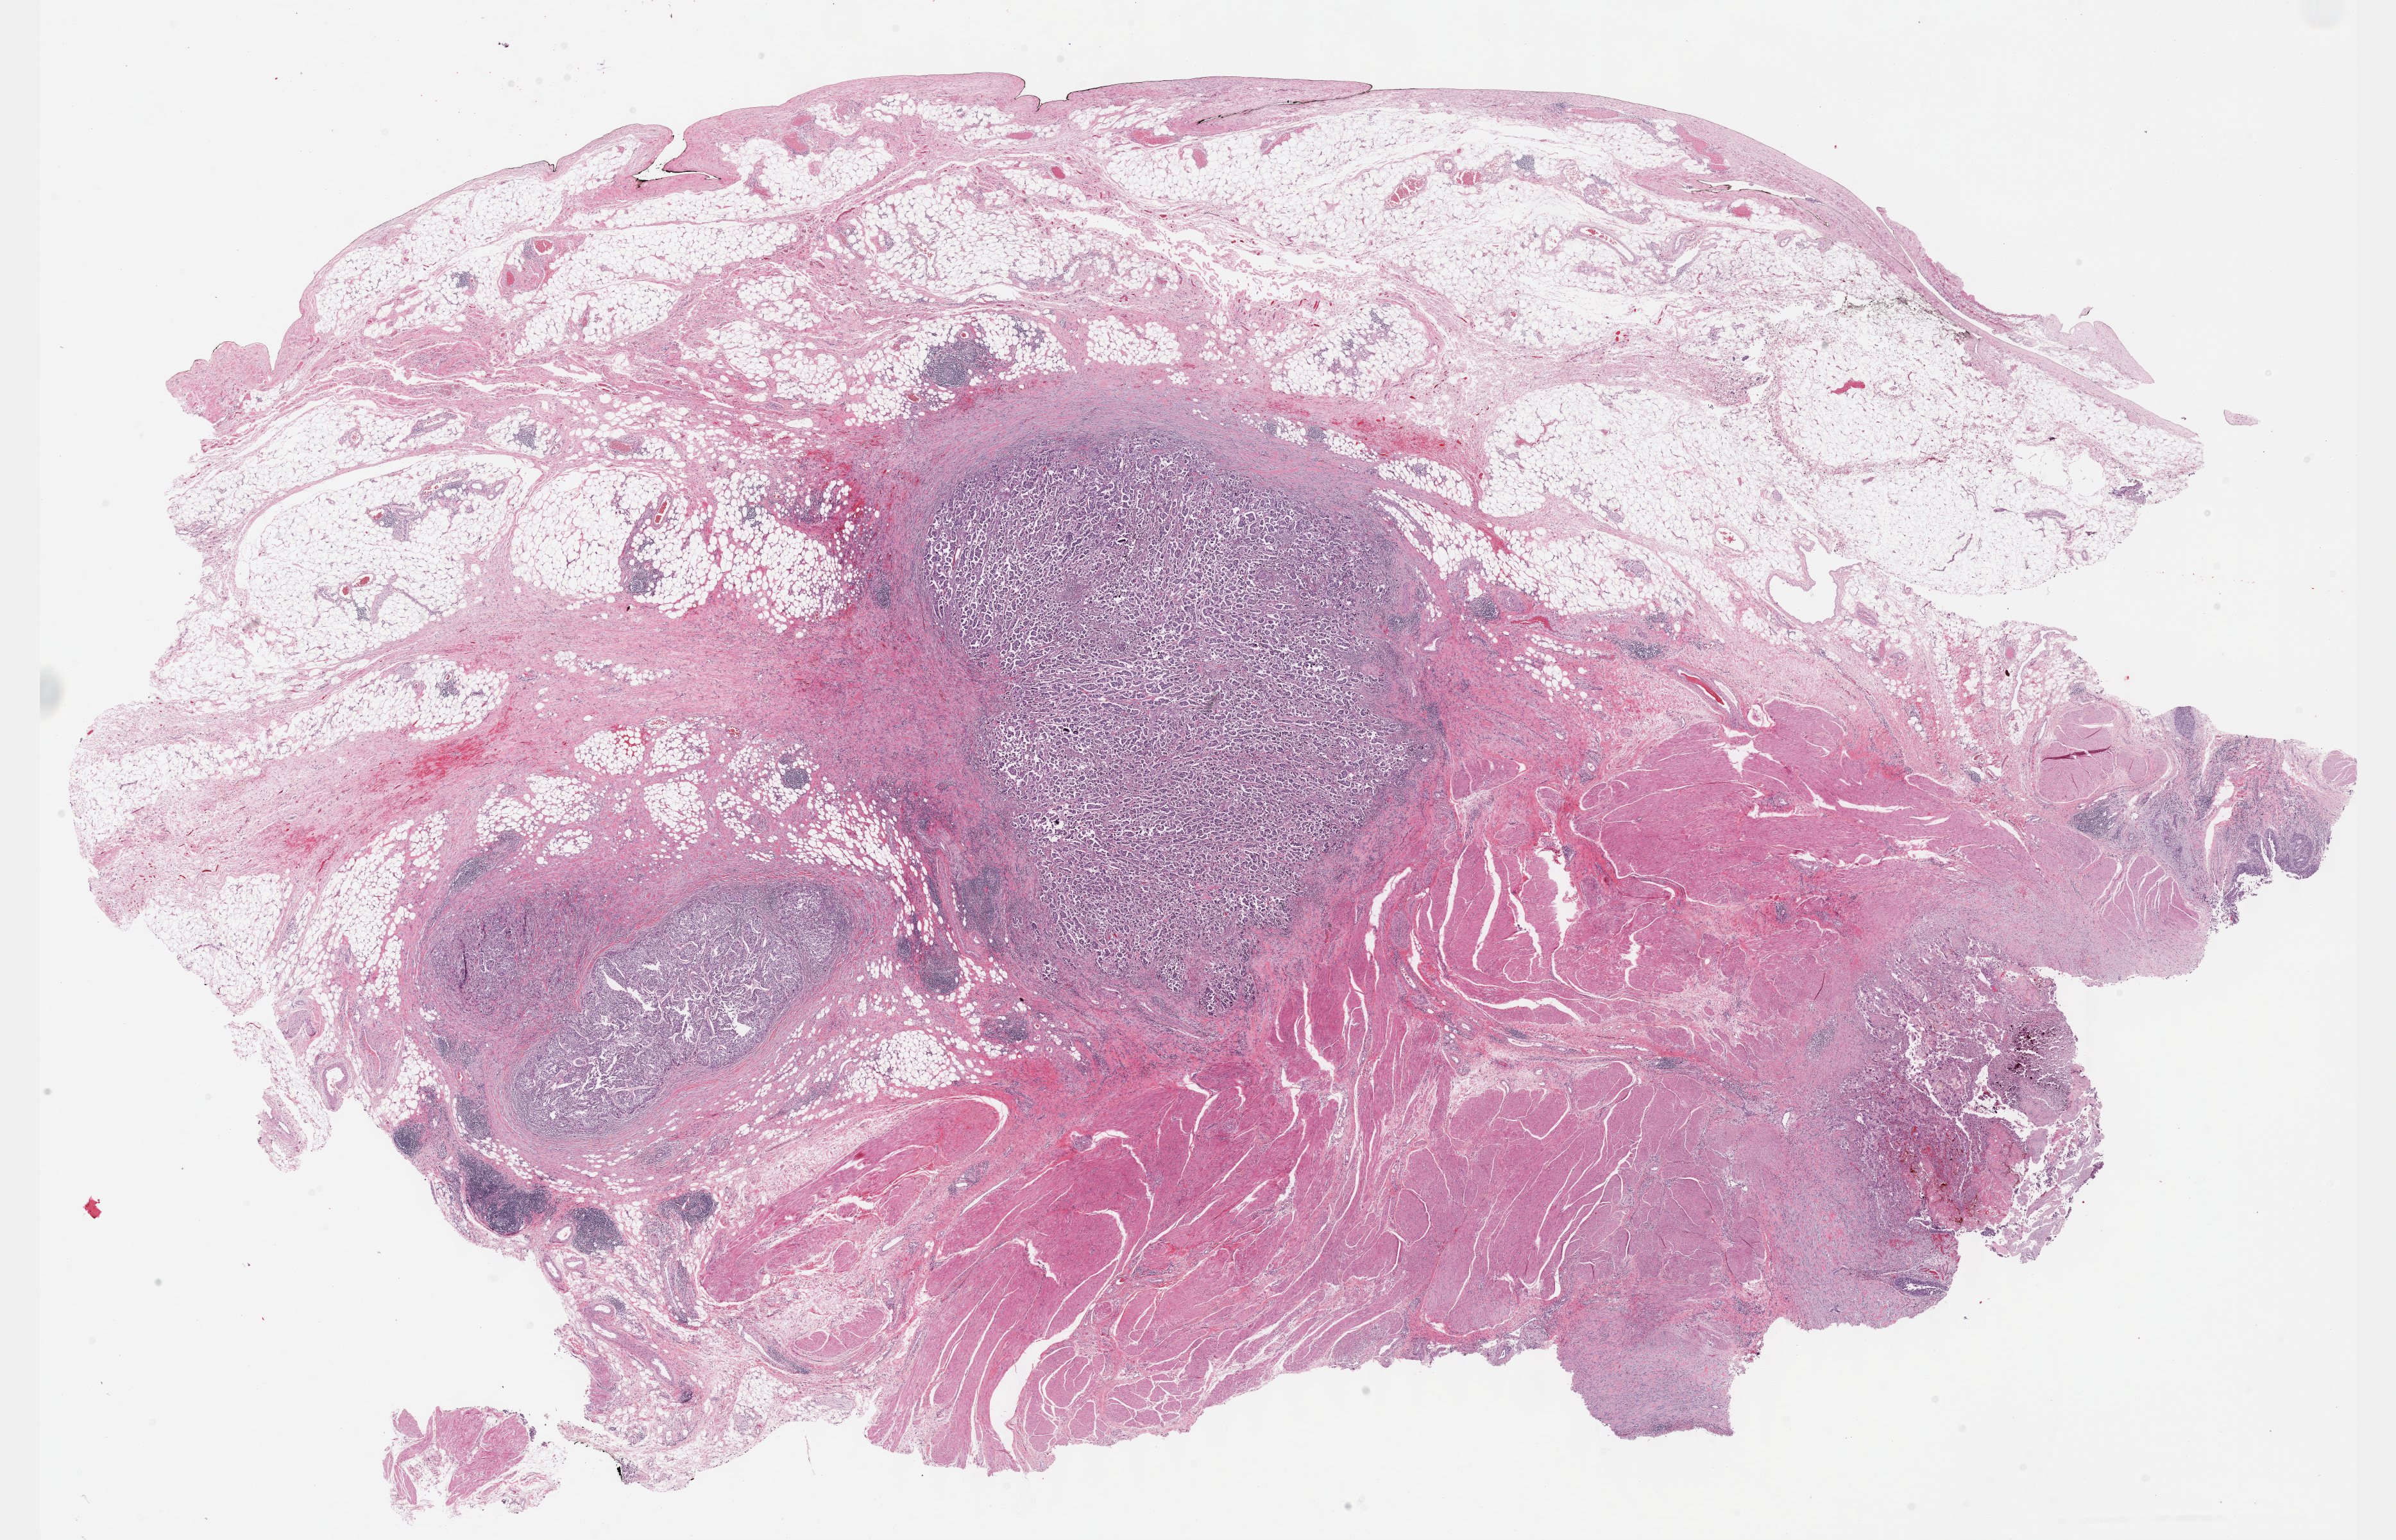
Hematoxylin and eosin (H&E) stained whole-slide image — whole scanned area (about 30.2 x 19.4 mm) shown as a low-resolution overview. Formalin-fixed paraffin-embedded (FFPE) diagnostic section. Primary tumour sample from the bladder. Male, age 72 years at initial diagnosis. Histologic grade: high grade.
* AJCC pathologic stage: IV (7th edition)
* pathologic diagnosis: Transitional cell carcinoma